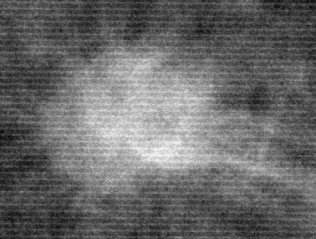
Region of interest cut from a scanned film mammogram (one marked finding), left breast, CC view, BI-RADS breast density category 1 (scale 1–4).
- Marked abnormality: mass, shape round, margins spiculated; BI-RADS assessment category 5; subtlety rating 5 on a 1 (subtle) to 5 (obvious) scale; pathology (as recorded): malignant.